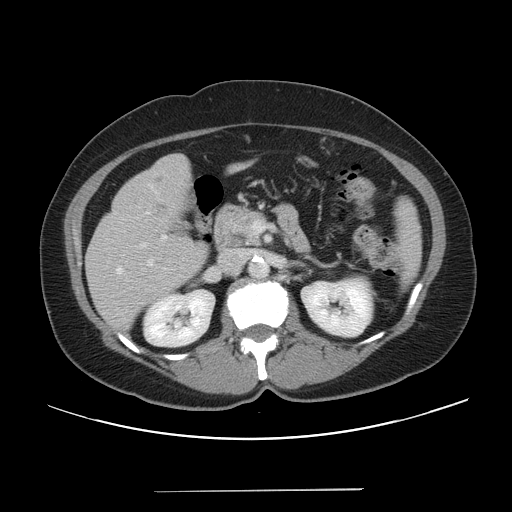
Contrast-enhanced abdominal CT, one axial slice; intravenous contrast given; soft-tissue window (W 400 / L 40 HU); 5 mm slice thickness; 512 × 512 image matrix, field of view 419 × 419 mm. Female patient, age 54 years. From the clinical record (not read from this slice): diagnosis: colorectal cancer liver metastases, imaged before liver resection; multiple liver metastases: yes; largest metastasis: 3.2 cm; disease in both lobes: yes.
Annotated regions visible in this slice (outlined manually by an expert reader):
- hepatic veins: bounding box <117,262,152,273> (left, top, right, bottom; pixels)
- liver: <85,155,249,331>
- planned liver remnant (the part of the liver to remain after resection): <159,155,250,191>
- portal vein (with intrahepatic branches): <162,221,265,240>